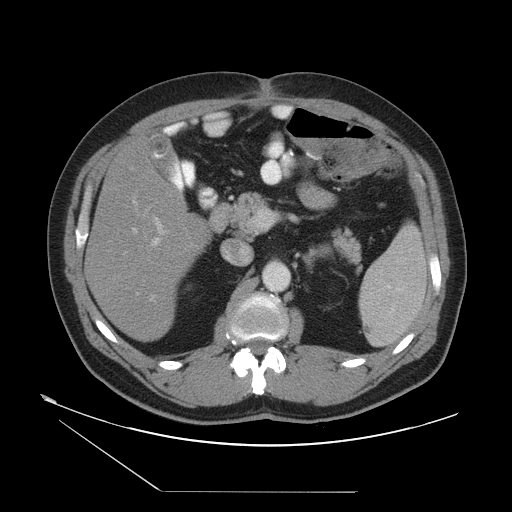
Contrast-enhanced abdominal CT, one axial slice. Position 24 of 55 along the scan axis. Reconstruction kernel STANDARD. Intravenous contrast given. Soft-tissue window (W 400 / L 40 HU). 512 × 512 image matrix, field of view 454 × 454 mm. Male patient, age 59 years. Case-level facts recorded for this patient, not image findings: diagnosis: colorectal cancer liver metastases, imaged before liver resection; multiple liver metastases: yes; largest metastasis: 0.3 cm; disease in both lobes: yes.
Annotated regions visible in this slice (manually delineated by an expert):
- hepatic veins: bounding box [x1, y1, x2, y2] px = [123, 197, 146, 295]
- liver: [88, 138, 211, 340]
- planned liver remnant (the part of the liver to remain after resection): [88, 138, 210, 341]
- portal vein (with intrahepatic branches): [149, 218, 166, 302]